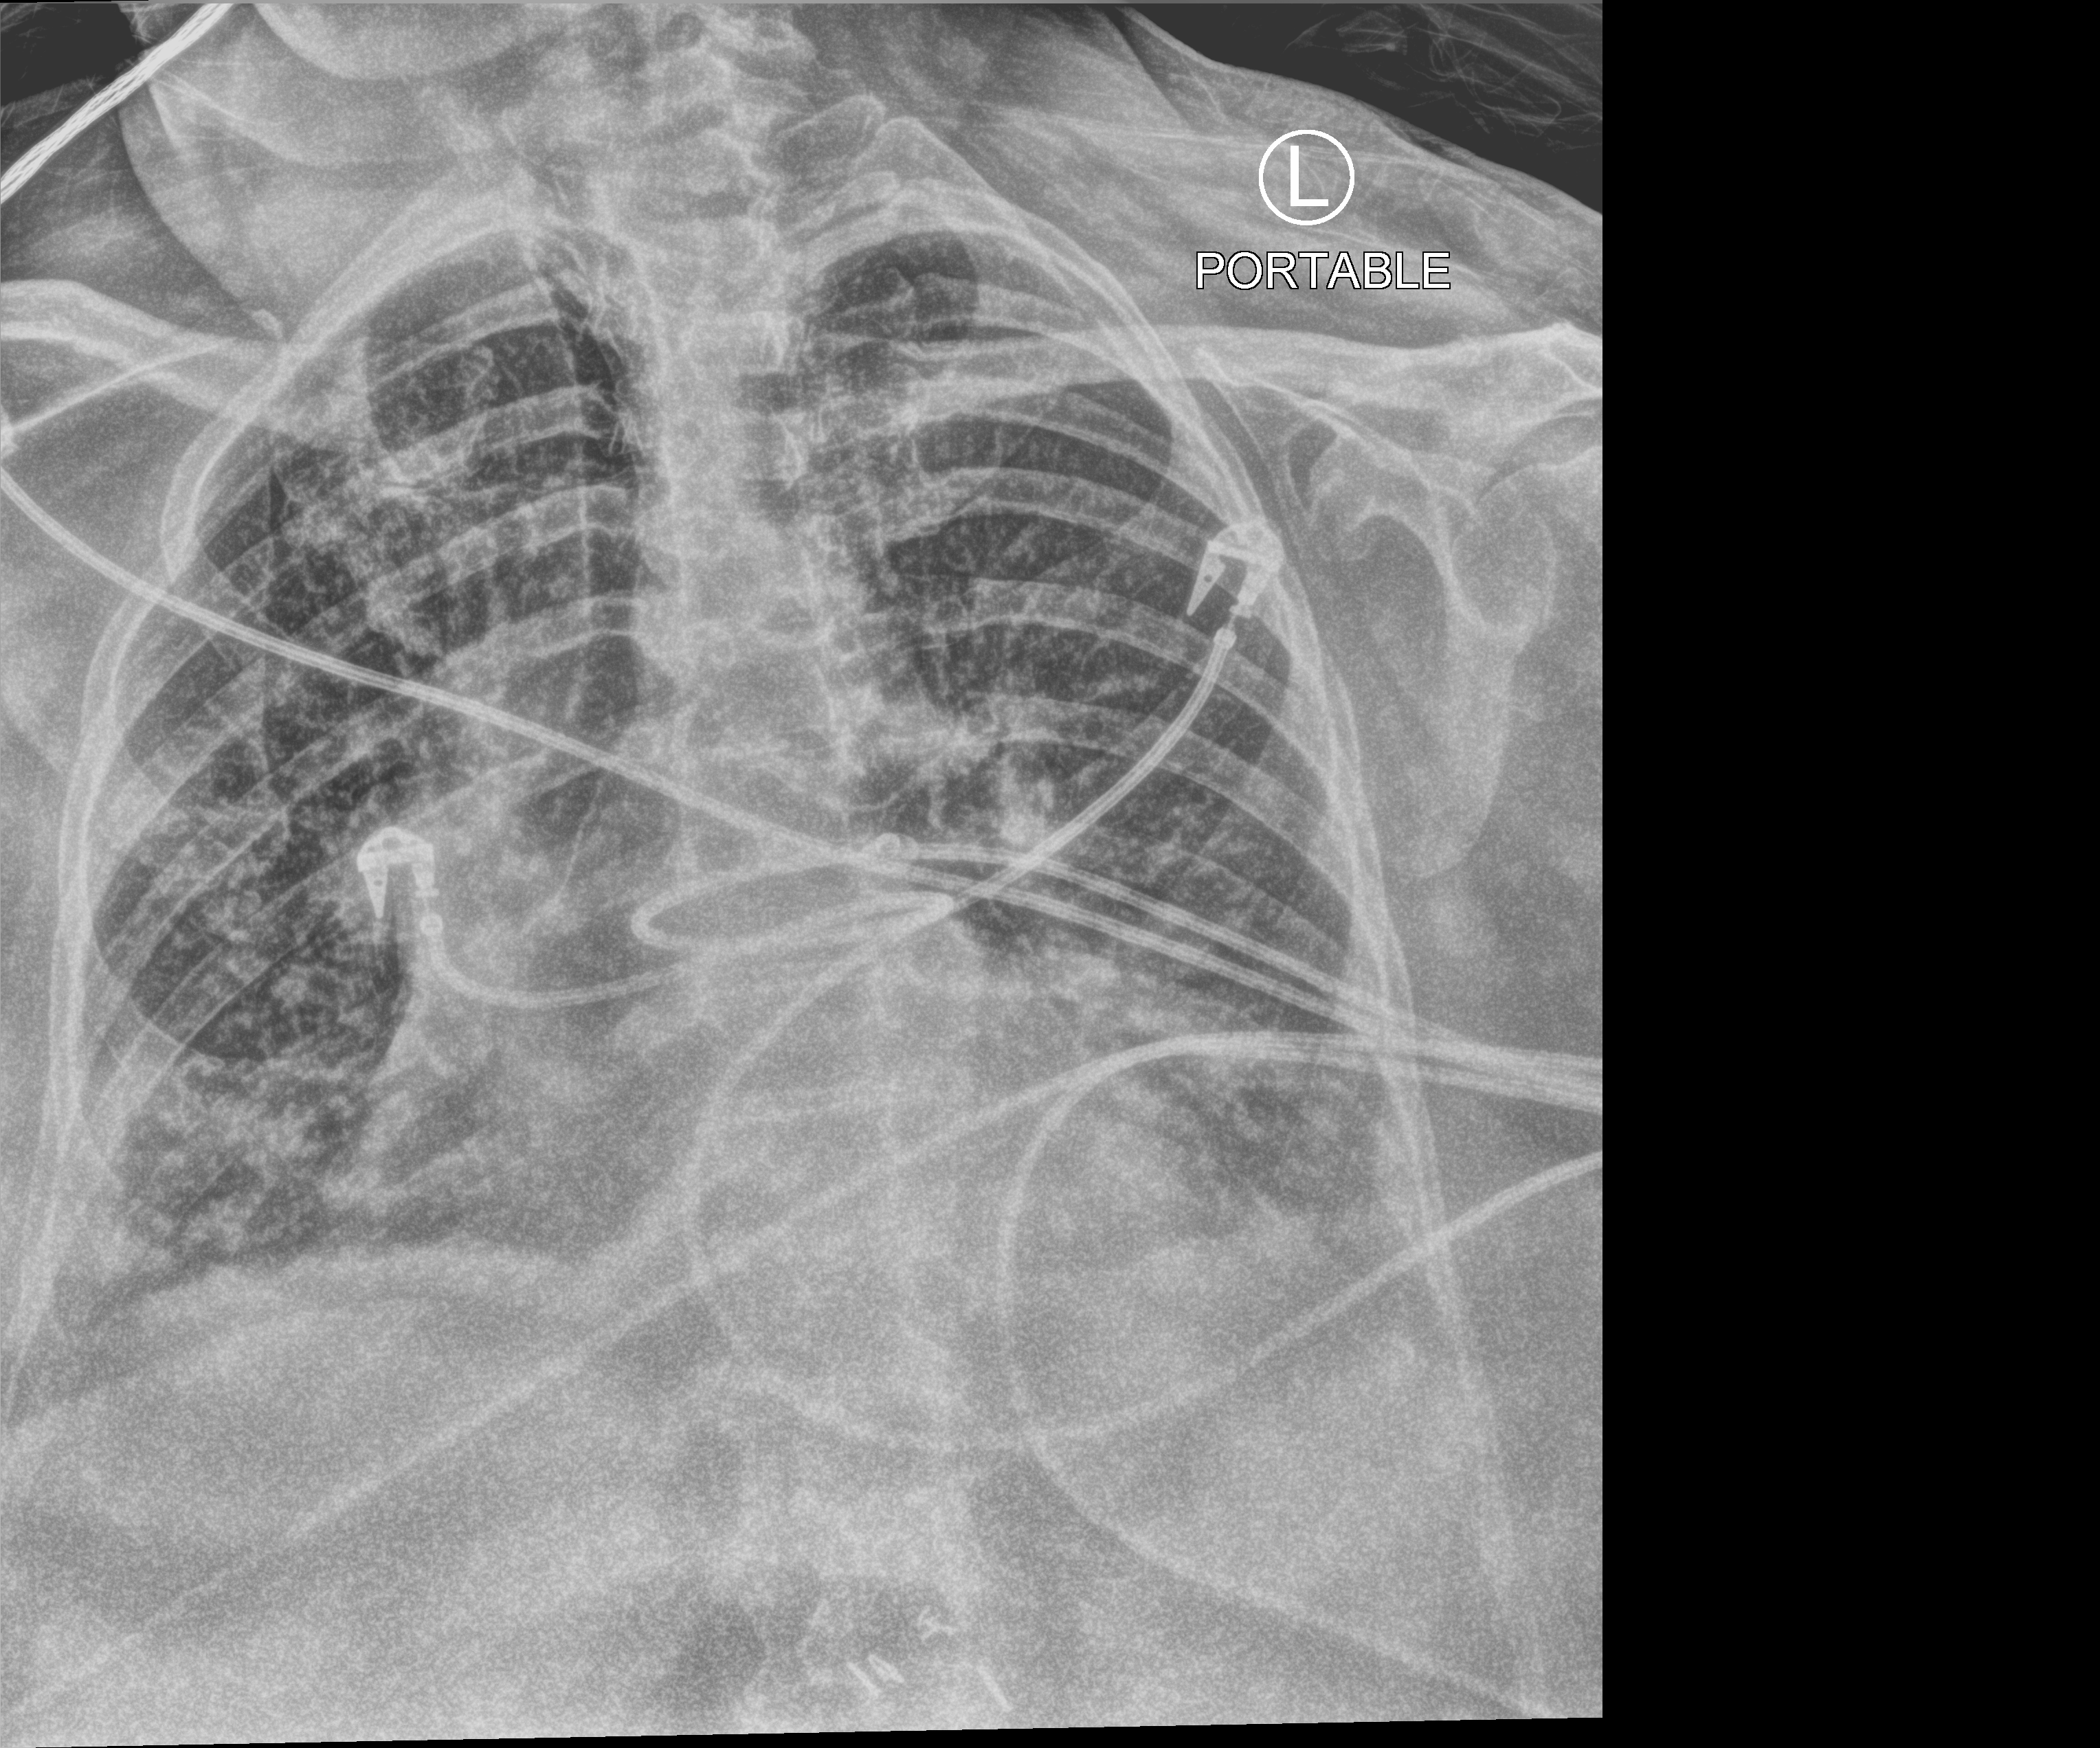
Portable chest radiograph; anteroposterior (AP) projection. Patient hospitalised with COVID-19; female, aged 75–90 years.
Hospital-stay facts (about this admission, not read from this image; timing relative to this image not recorded): diabetes (admission record): no; length of hospital stay: 19 days; mechanically ventilated during this hospital stay: no.